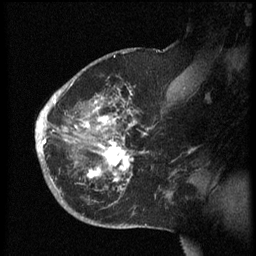
Breast MRI (dynamic contrast-enhanced), one sagittal slice; slice 40 of 60 in the series (ordered by position); dynamic contrast-enhanced series, image 2 of 3 at this slice position (ordered by acquisition); 1.5 T; TE 4.2 ms, TR 8.4 ms; 256 × 256 image matrix, field of view 200 × 200 mm. Female patient, age 38 years. From the clinical record (not read from this slice): setting: breast cancer imaged before/during neoadjuvant chemotherapy; receptor status: HER2-positive.
Structures marked on this image (semi-automatic segmentation, software-assisted and operator-edited):
- analysis volume of interest (the breast-tissue region the enhancement analysis was run in; not a lesion): box from (x=36, y=74) to (x=173, y=202) px
- tumour enhancement mask (voxels above the 70 % enhancement threshold inside the analysis volume of interest): (x=36, y=91)–(x=149, y=191)